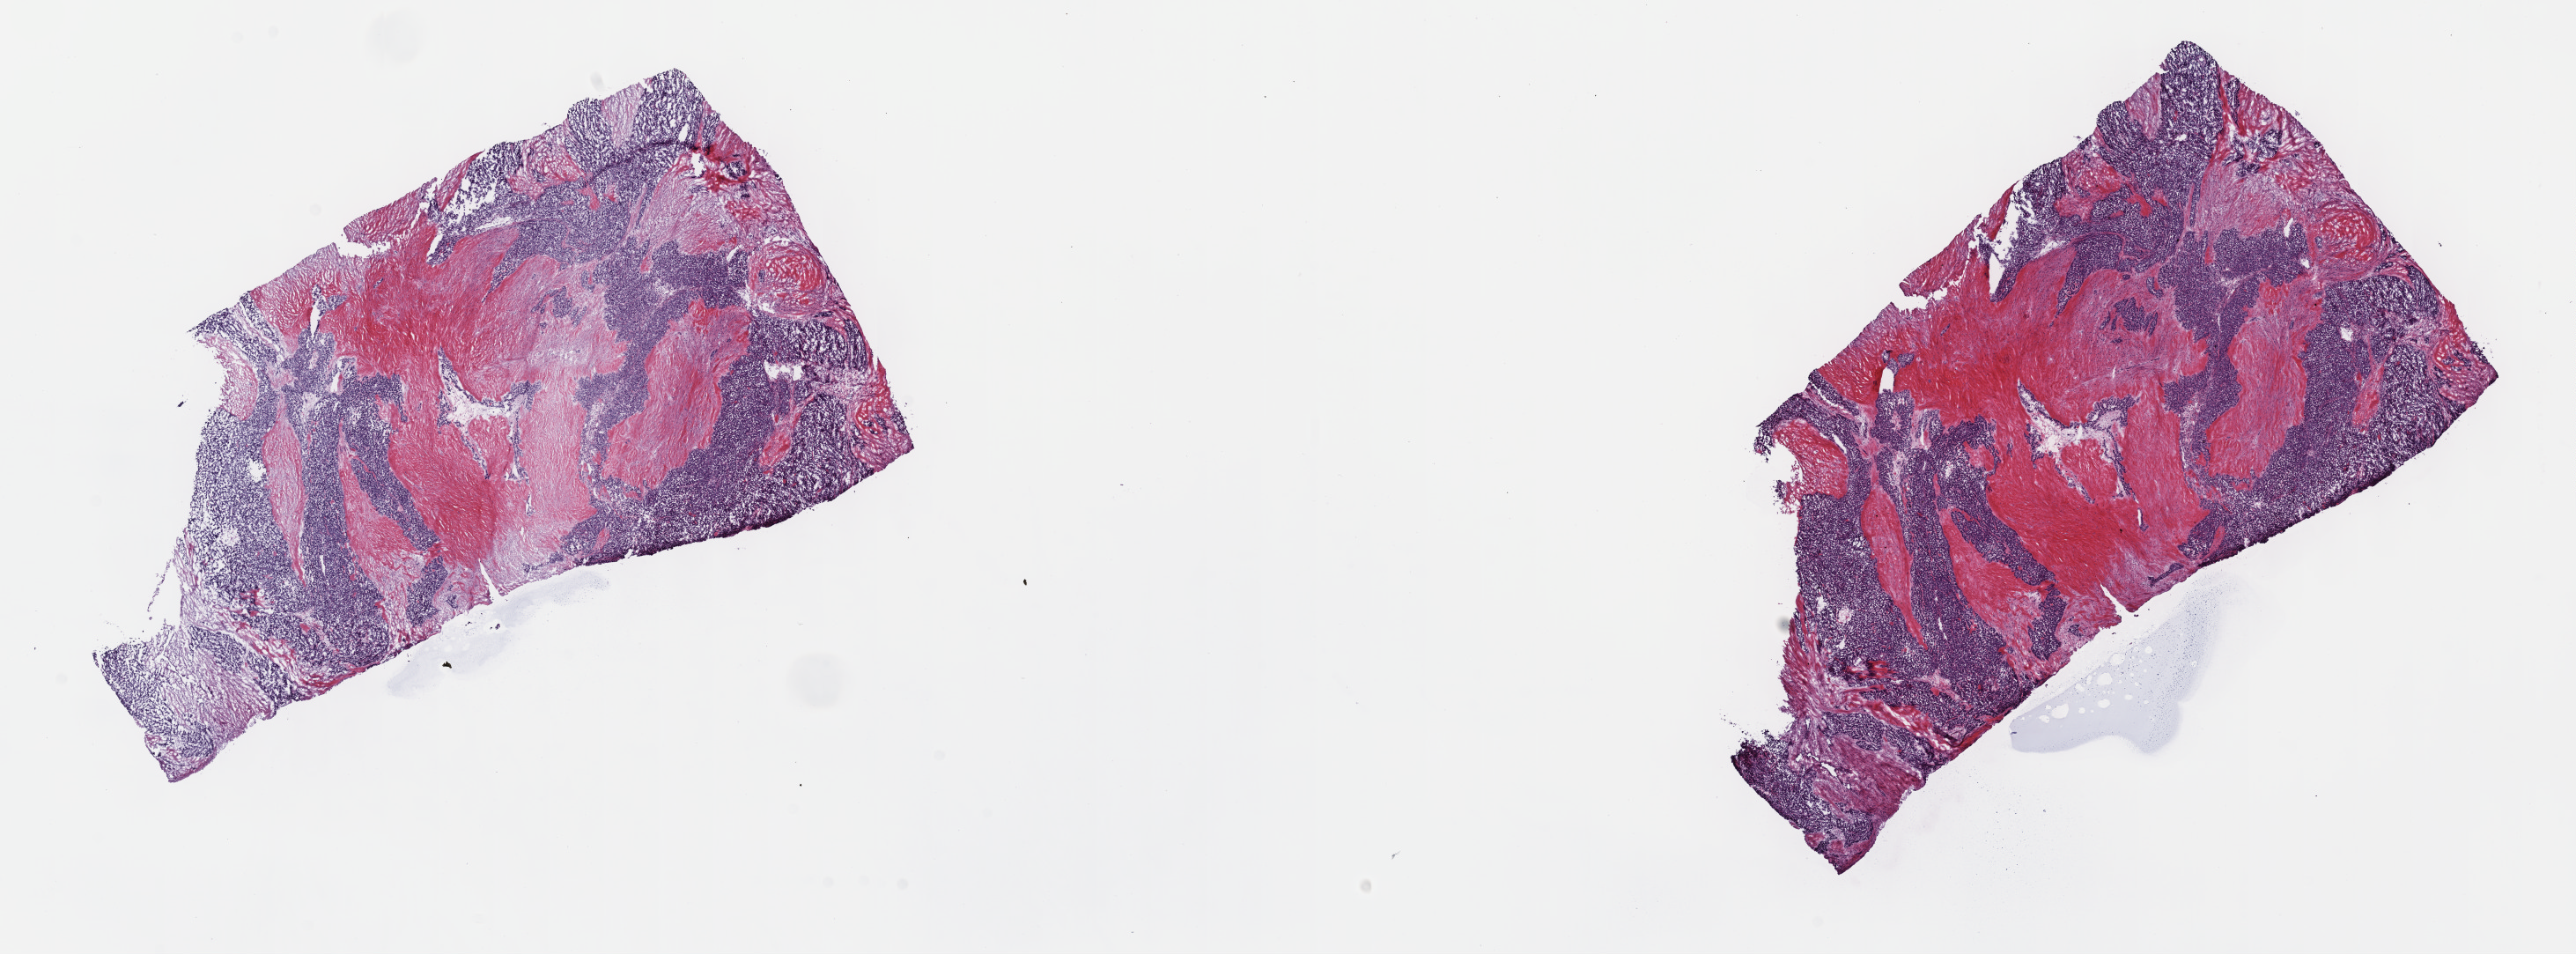
Hematoxylin and eosin (H&E) stained whole-slide image, whole scanned area (about 23.7 x 8.8 mm, acquisition: 40x scan) shown as a low-resolution overview, frozen section from the top of the tissue portion, pancreas, primary tumour sample. Patient: female, age at initial diagnosis 59 years. Histologic grade: G1 (well differentiated). Composition of this section per pathologist review: tumour cells 100%, tumour nuclei 90%, normal cells 0%, stromal cells 0%, necrosis 0%. Infiltration values recorded for this section: lymphocyte infiltration 0%, monocyte infiltration 0%, neutrophil infiltration 0%.
Histologic diagnosis: Neuroendocrine carcinoma, NOS. Lymph nodes positive (case pathology): 0 of 16 examined. AJCC pathologic stage: IB (7th edition).